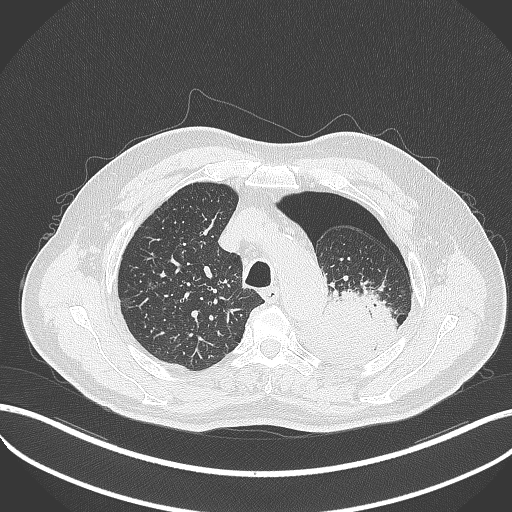
Chest CT, one axial slice; slice 393 of 464 in the series (ordered by position); 120 kVp; lung window (W 1500 / L -600 HU); 1 mm slice thickness; 512 × 512 image matrix, field of view 400 × 400 mm. Male patient, age 76 years. From the clinical record (not read from this slice): clinical TNM (as recorded): T3 N0 M1b.
Outlined on this slice (bounding box drawn by a radiologist):
- lung tumour (recorded histology: adenocarcinoma): bounding box <308,281,401,361> (left, top, right, bottom; pixels)